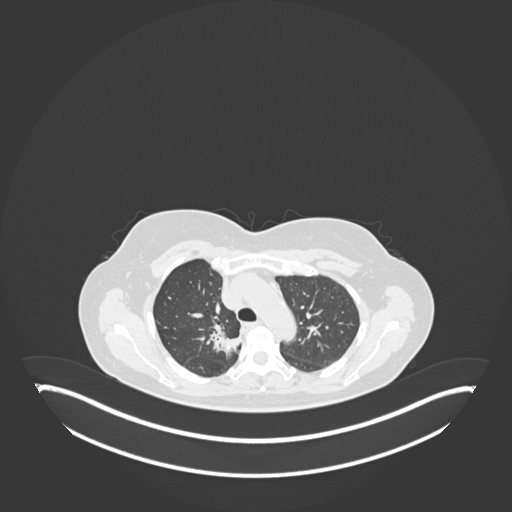
Chest CT, one axial slice; position 130 of 181 along the scan axis; reconstruction kernel B30f; lung window (W 1500 / L -600 HU); 1 mm slice thickness; 512 × 512 image matrix, field of view 500 × 500 mm. Female patient, age 65 years. Case-level facts recorded for this patient, not image findings: clinical TNM (as recorded): T1b N0 M0.
Outlined on this slice (rectangle marked by the reading radiologist):
- lung tumour (recorded histology: adenocarcinoma): bounding box (x1, y1, x2, y2) in pixels: (207, 327, 240, 358)